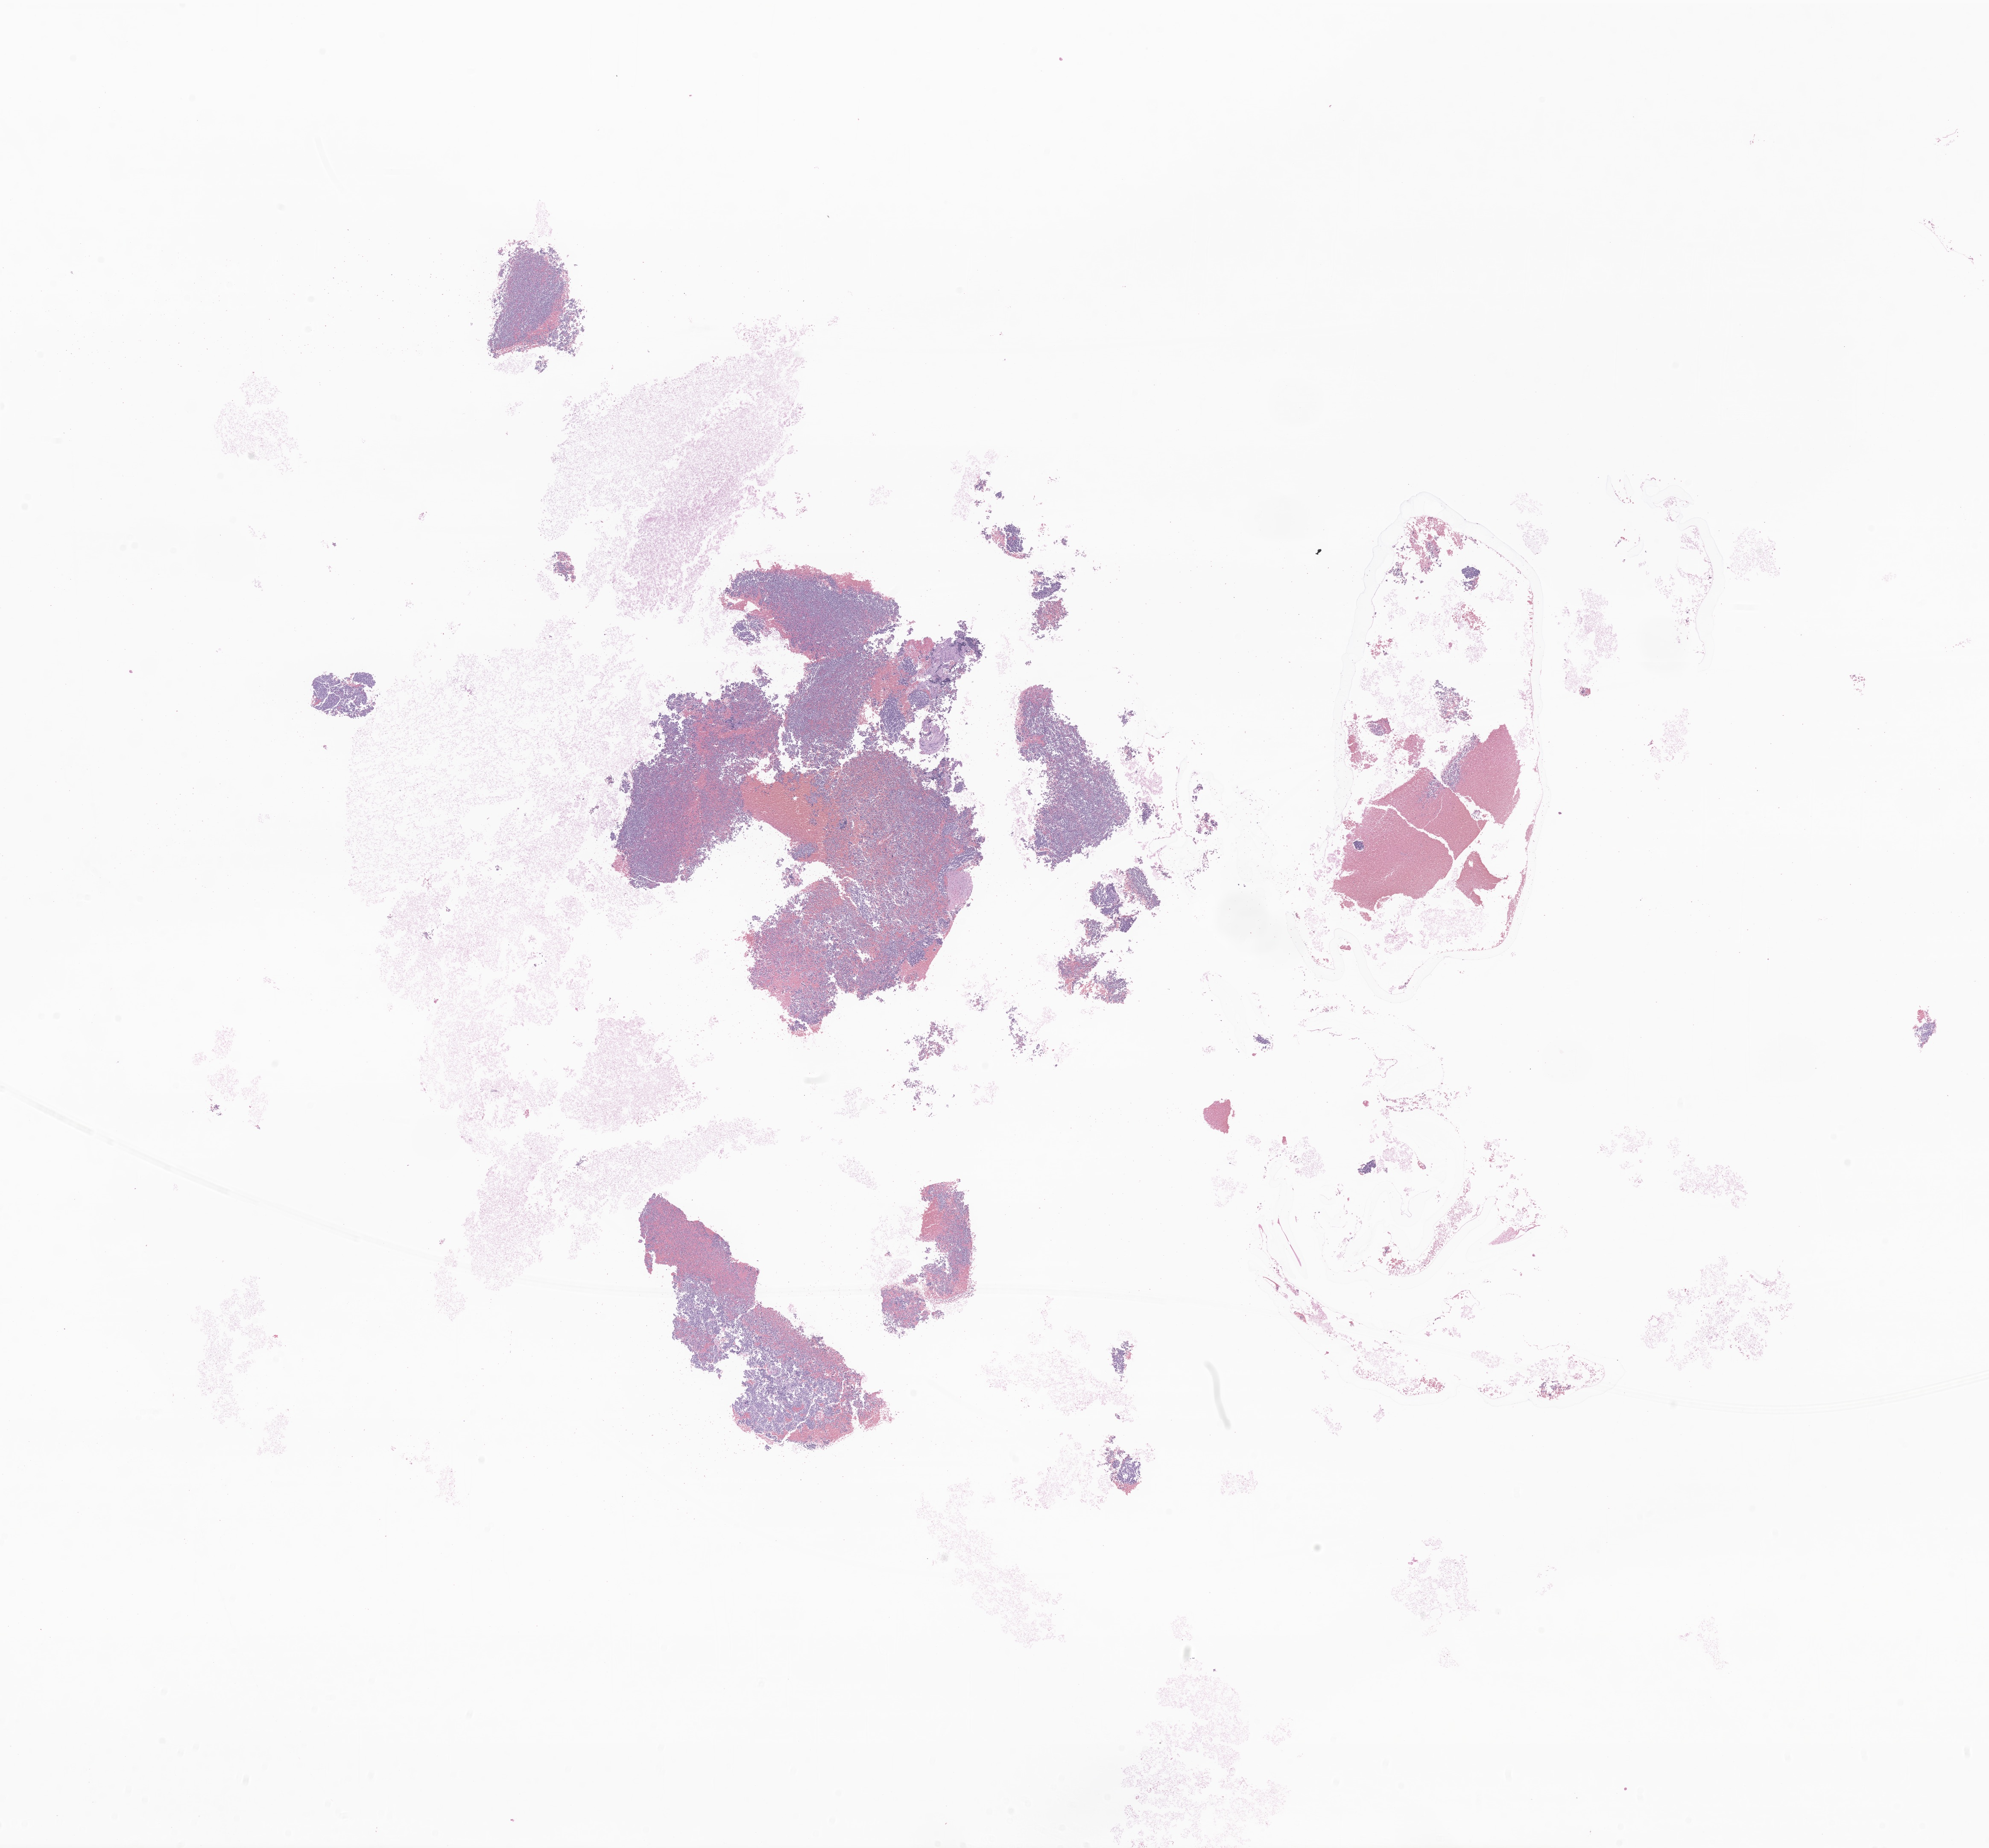
Digitized H&E-stained section of tumor tissue from the adrenal gland, a low-resolution overview of the entire scanned area, about 19.6 x 18.2 mm. Formalin-fixed, paraffin-embedded (FFPE) tissue. Patient: male, age 749 days.
Recorded diagnosis: Neuroblastoma, NOS.